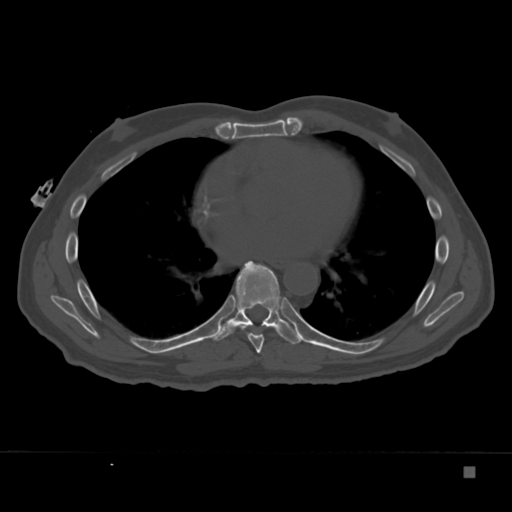
CT including the spine, one axial slice. Slice 214 of 332 in the series (ordered by position). Bone window (W 1800 / L 400 HU). 1.5 mm slice thickness. 512 × 512 image matrix, field of view 389 × 389 mm. Patient: male, 72 years. From the clinical record (not read from this slice): primary cancer: skeletal.
Structures marked on this image (semi-automatic segmentation, software-assisted and operator-edited):
- T7 vertebra: bounding box <239,325,265,353> (left, top, right, bottom; pixels)
- T8 vertebra: <211,260,304,345>